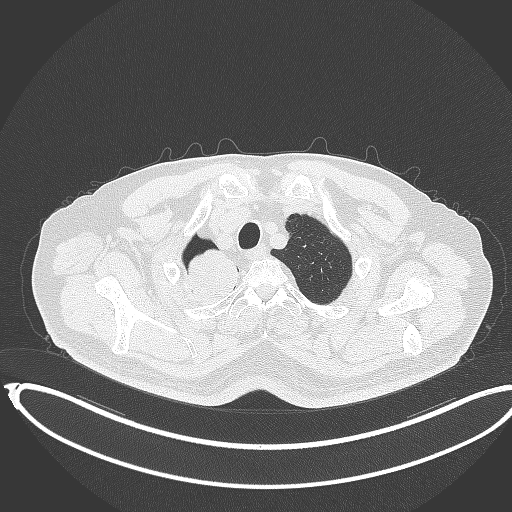
Chest CT, one axial slice. Slice 331 of 403 in the series (ordered by position). 120 kVp. Lung window (W 1500 / L -600 HU). 1 mm slice thickness. 512 × 512 image matrix, field of view 436 × 436 mm. Male patient, age 68 years. Case-level facts recorded for this patient, not image findings: clinical TNM (as recorded): T2a N0 M0.
Outlined on this slice (bounding box drawn by a radiologist):
- lung tumour (recorded histology: adenocarcinoma): box from (x=175, y=242) to (x=247, y=317) px